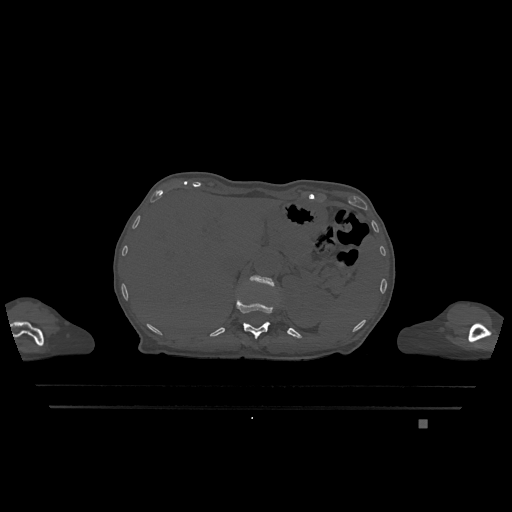
CT including the spine, one axial slice; slice 523 of 1317 in the series (ordered by position); bone window (W 1800 / L 400 HU); 0.5 mm slice thickness; 512 × 512 image matrix, field of view 500 × 500 mm. Female patient, age 74 years. From the clinical record (not read from this slice): primary cancer: lung.
Structures marked on this image (semi-automatic segmentation, software-assisted and operator-edited):
- L1 vertebra: bounding box <249,275,275,287> (left, top, right, bottom; pixels)
- T12 vertebra: <236,297,274,339>